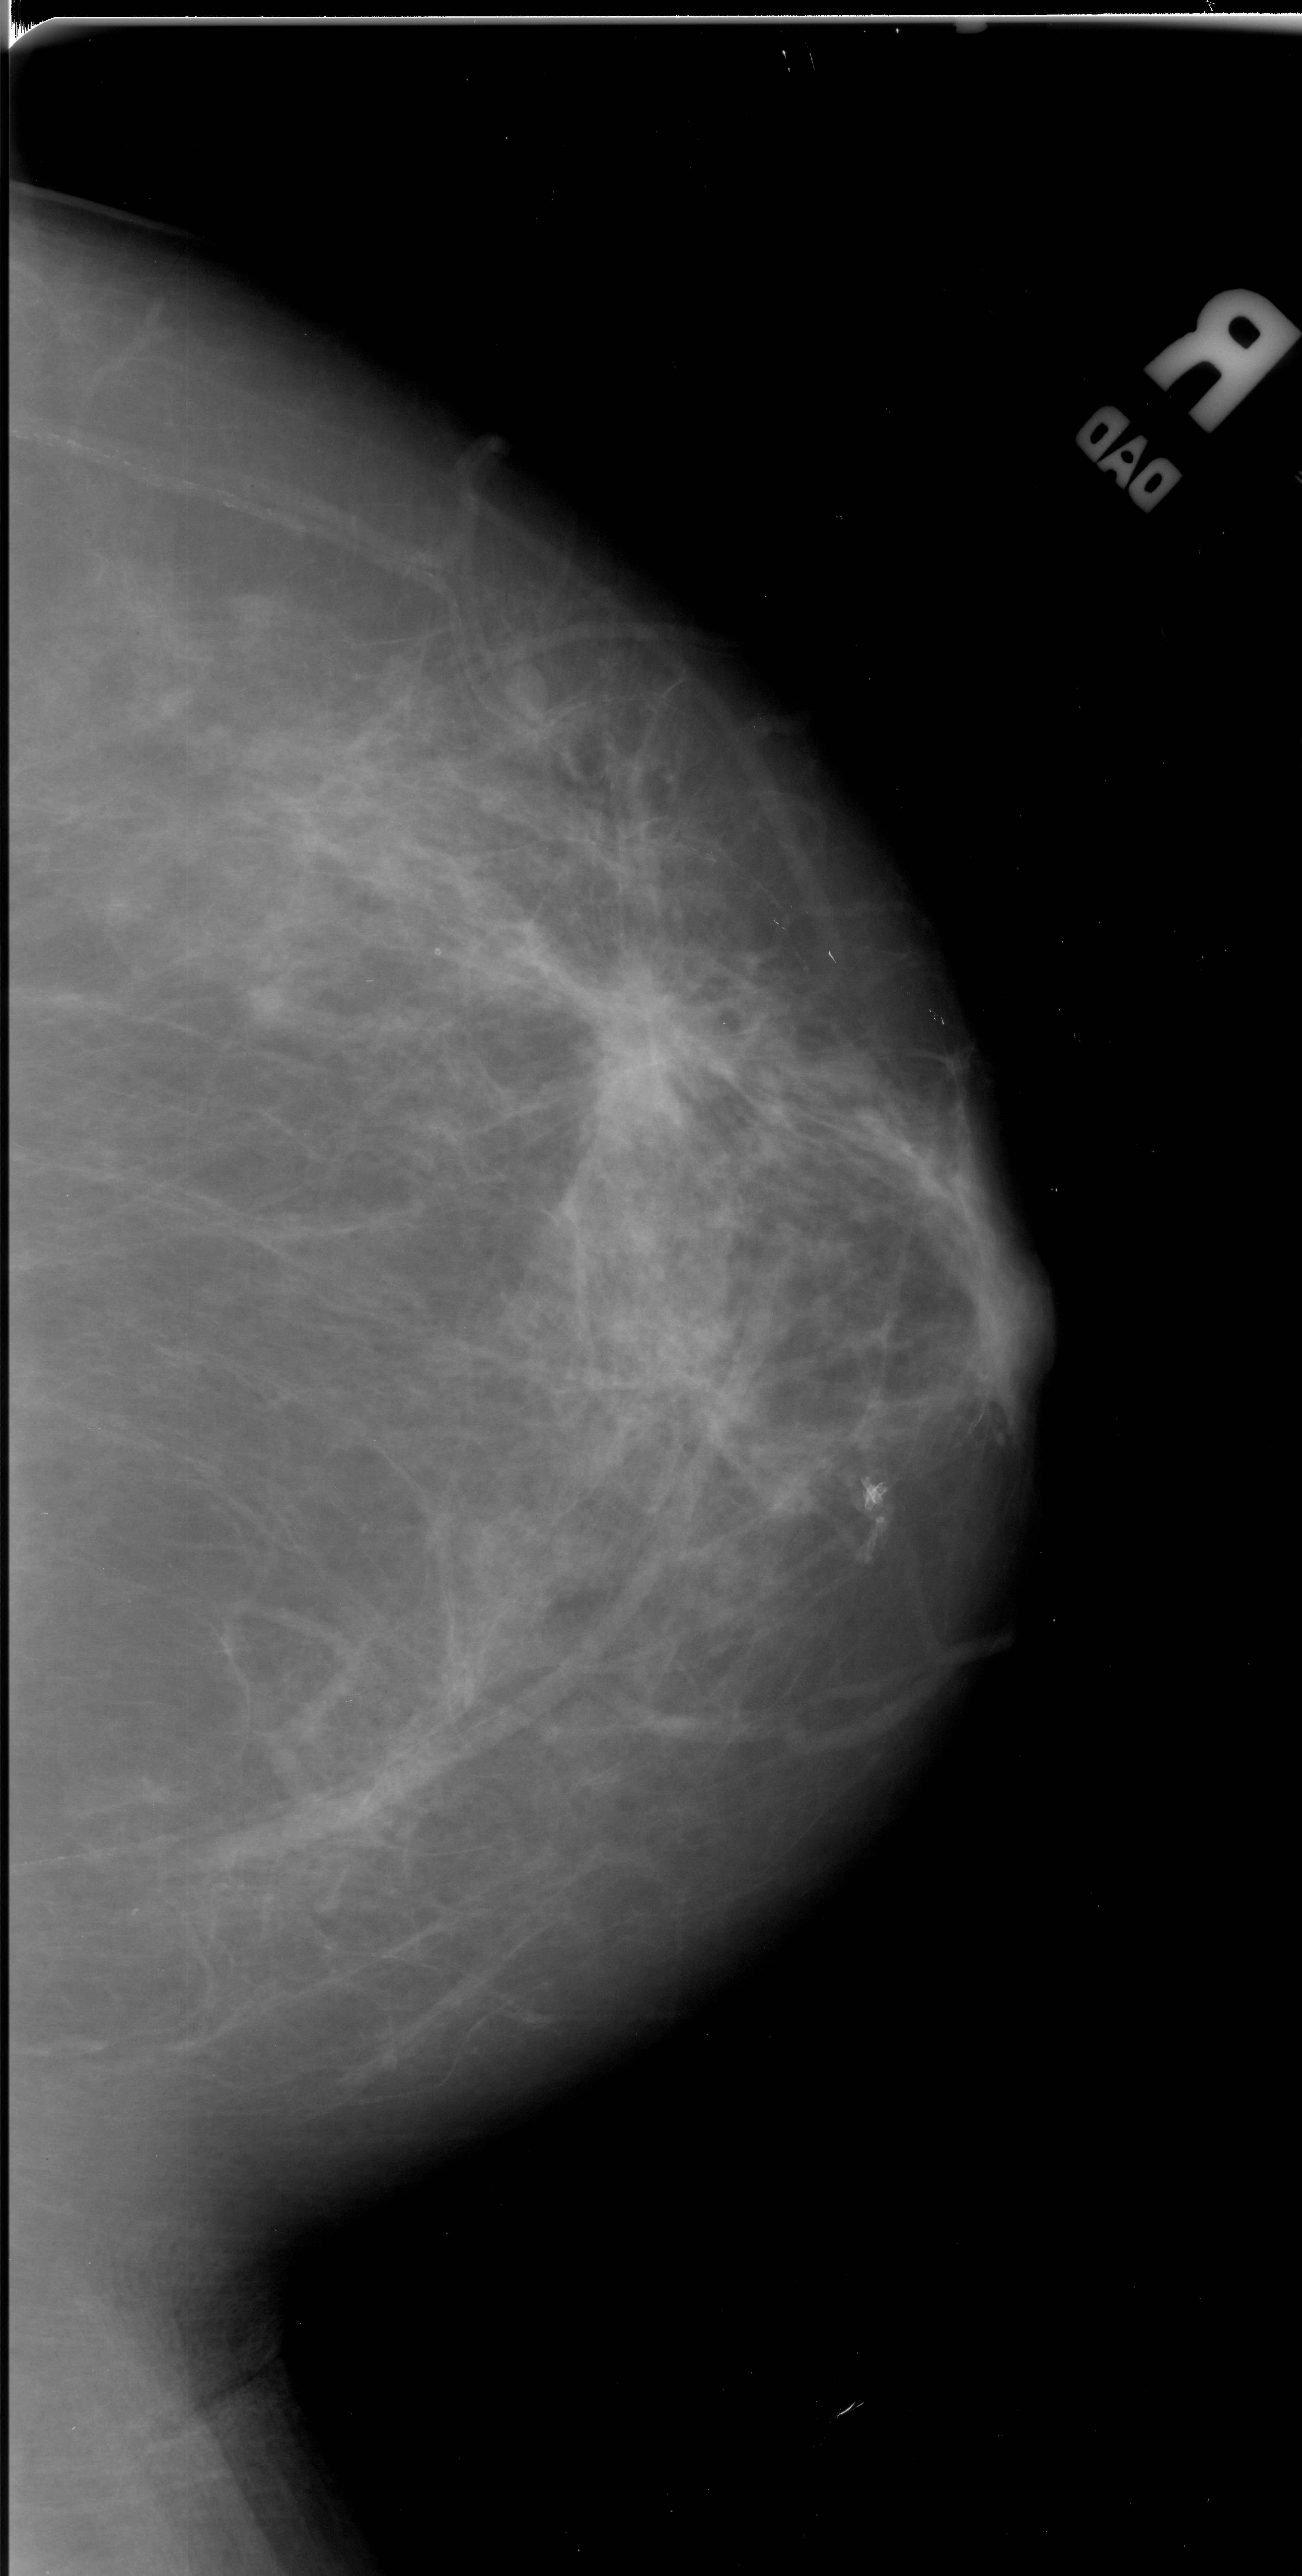
Mammogram (digitized film). Right breast. Craniocaudal (CC) view. BI-RADS breast density category 2 (scale 1–4). 1302 × 2576 image matrix.
Marked abnormalities (boxes around the expert regions of interest):
- mass, shape irregular, margins spiculated; BI-RADS assessment category 5; subtlety rating 5 on a 1 (subtle) to 5 (obvious) scale; pathology (as recorded): malignant: box from (x=559, y=952) to (x=707, y=1105) px